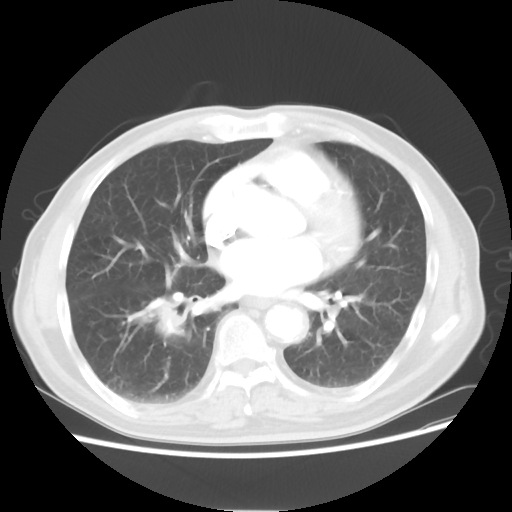
Chest CT, one axial slice; reconstruction kernel STANDARD; lung window (W 1500 / L -600 HU); 512 × 512 image matrix, field of view 360 × 360 mm. Patient: male, 74 years. From the clinical record (not read from this slice): clinical TNM (as recorded): T1c N1 M1.
Annotated regions visible in this slice (bounding box drawn by a radiologist):
- lung tumour (recorded histology: adenocarcinoma): bounding box [x1, y1, x2, y2] px = [120, 291, 196, 350]